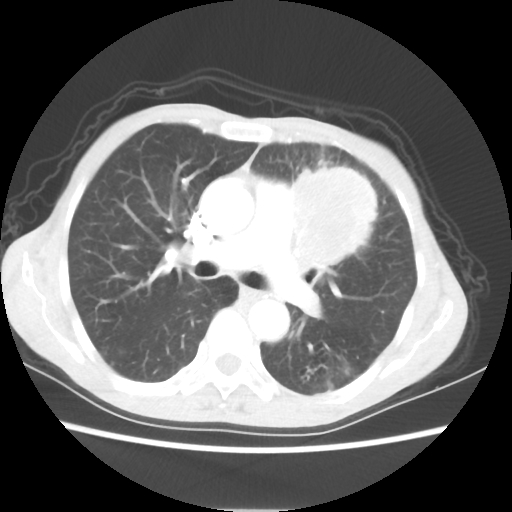
Chest CT, one axial slice; position 35 of 56 along the scan axis; 80 kVp; lung window (W 1500 / L -600 HU); 5 mm slice thickness; 512 × 512 image matrix, field of view 331 × 331 mm. Female patient, age 60 years. From the clinical record (not read from this slice): clinical TNM (as recorded): T4 N1 M0.
Outlined on this slice (bounding box drawn by a radiologist):
- lung tumour (recorded histology: adenocarcinoma): bounding box <286,157,381,273> (left, top, right, bottom; pixels)